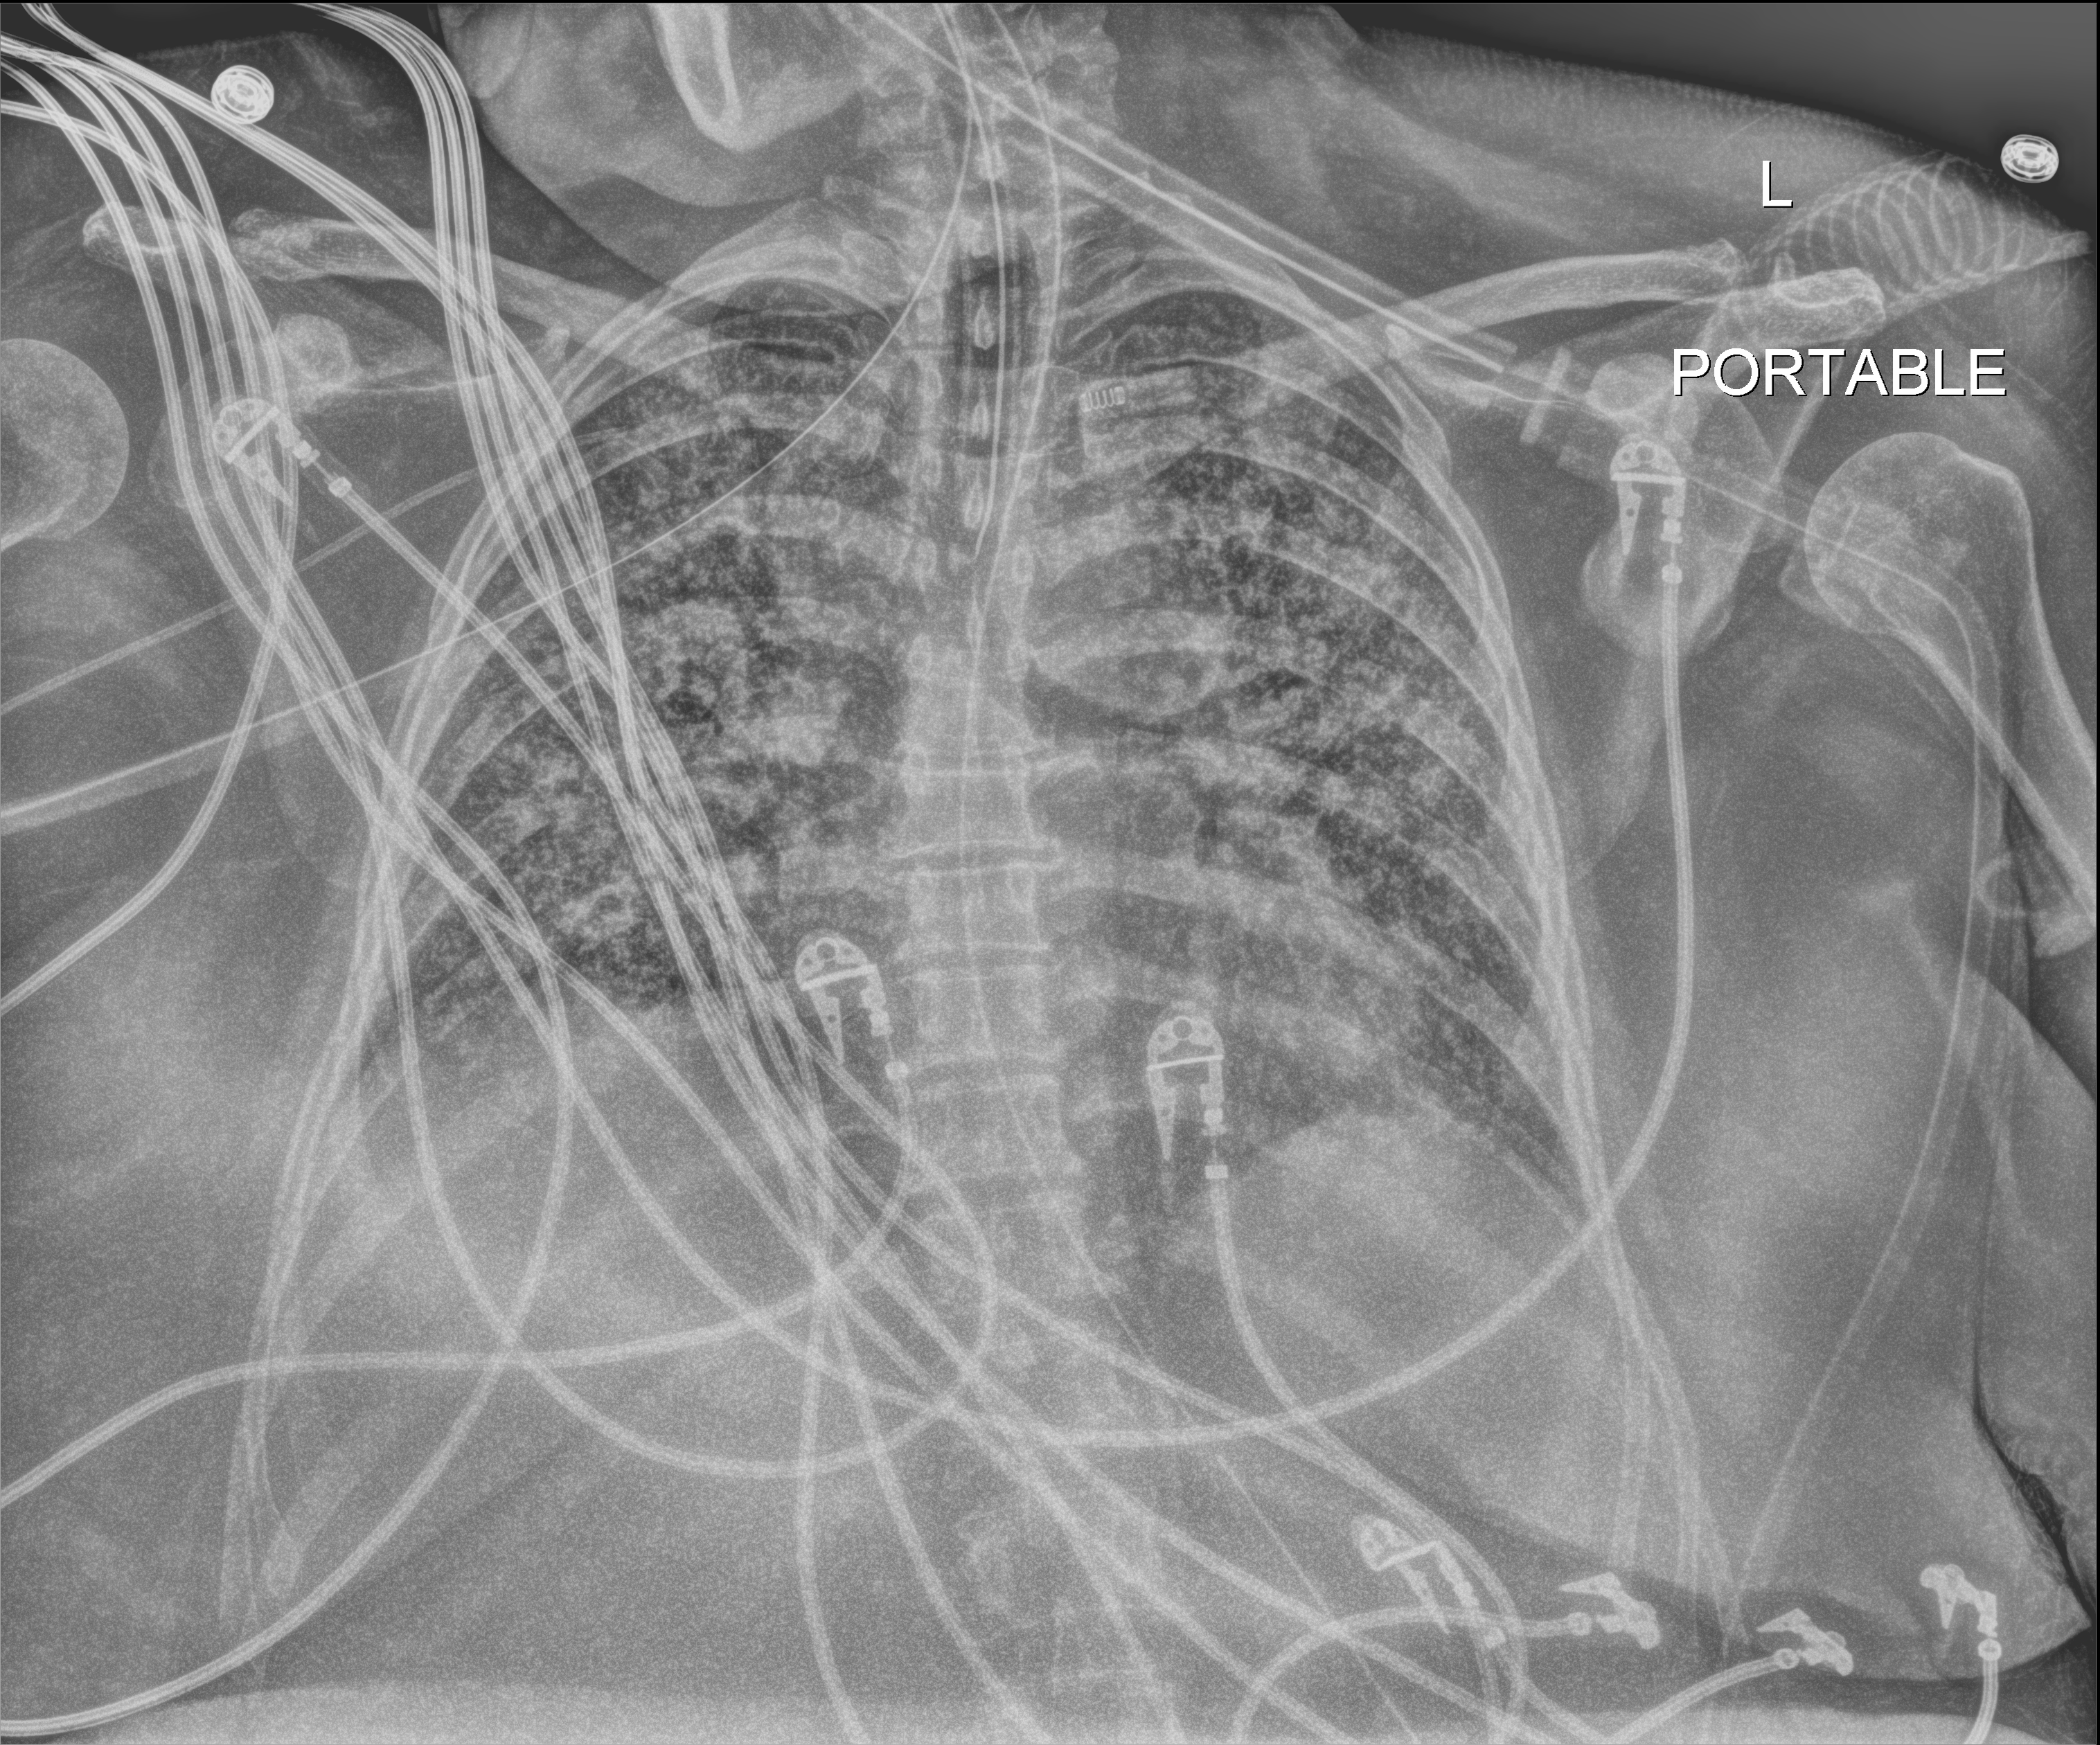
Portable chest radiograph. Patient hospitalised with COVID-19; female, aged 18–59 years.
Hospital-stay facts (about this admission, not read from this image; timing relative to this image not recorded):
- smoking status (admission record): never
- mechanically ventilated during this hospital stay: yes